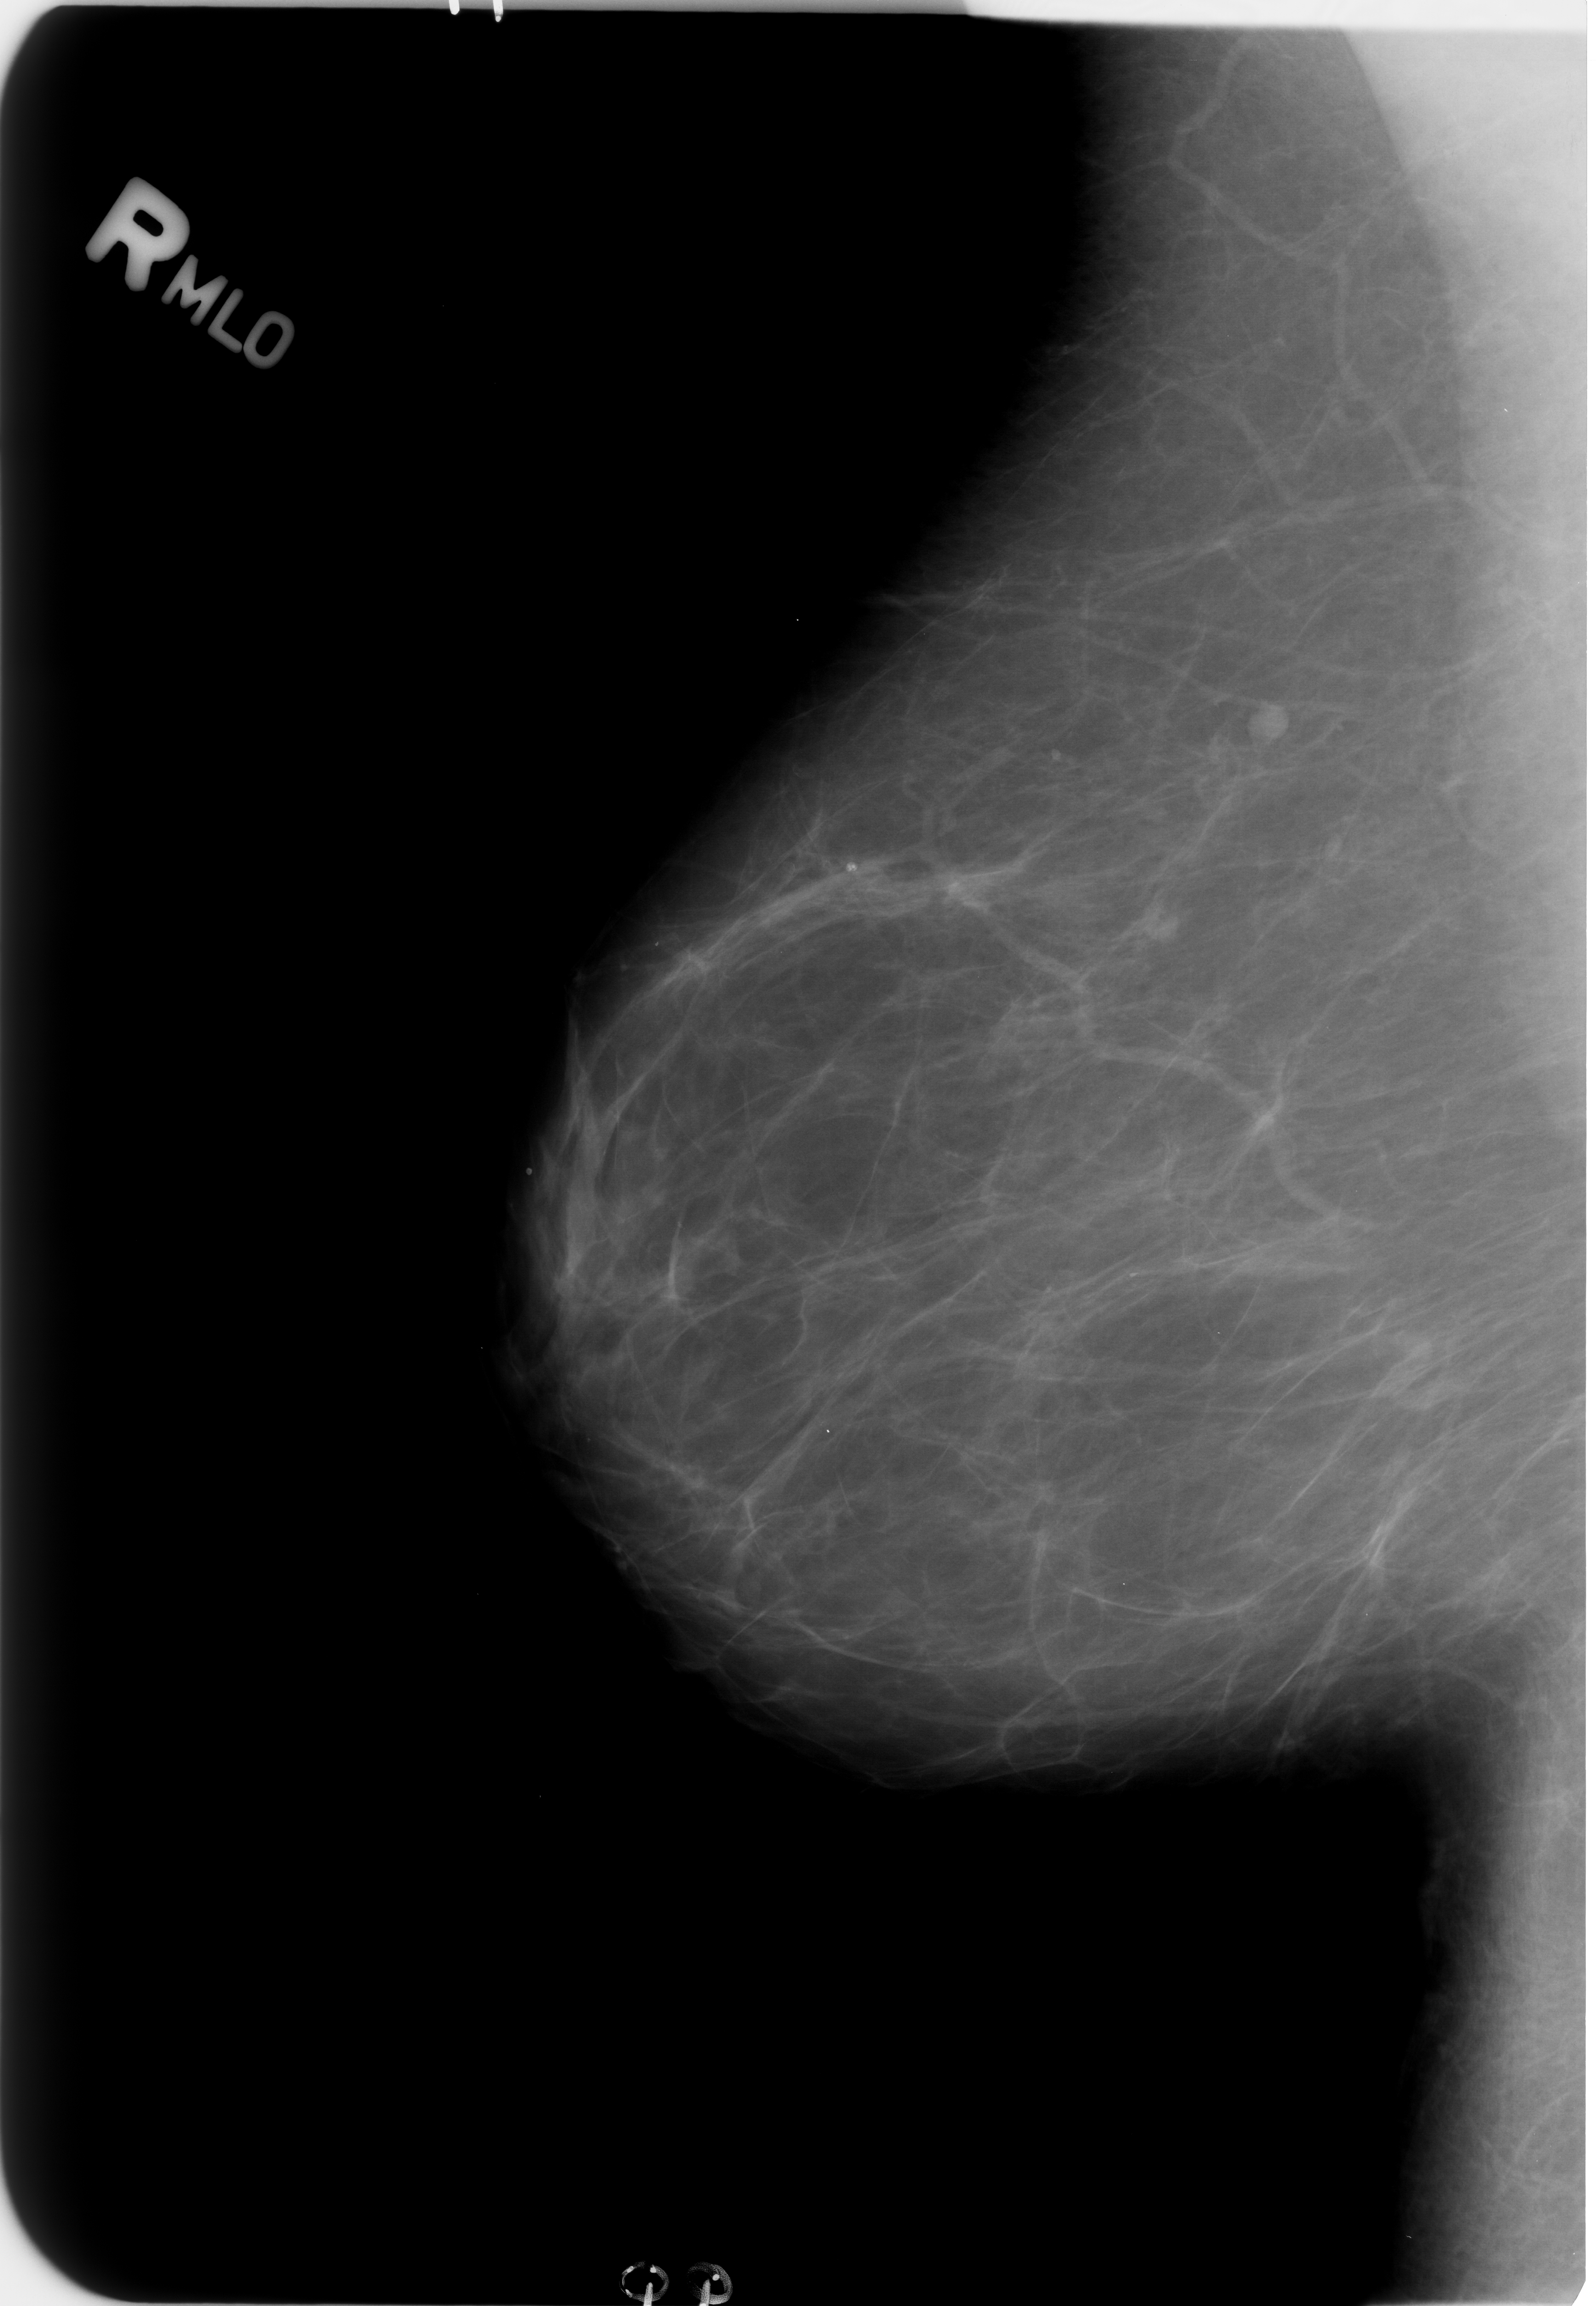
Mammogram (digitized film). Right breast. MLO view. BI-RADS breast density category 1 (scale 1–4). 1596 × 2306 image matrix.
Expert-marked regions of interest on this film, with their recorded descriptors:
- calcifications, morphology coarse; BI-RADS assessment category 2; subtlety rating 4 on a 1 (subtle) to 5 (obvious) scale; benign; no additional work-up was recommended (outcome (as recorded, no biopsy): benign without callback): bounding box [x1, y1, x2, y2] px = [508, 1148, 561, 1194]